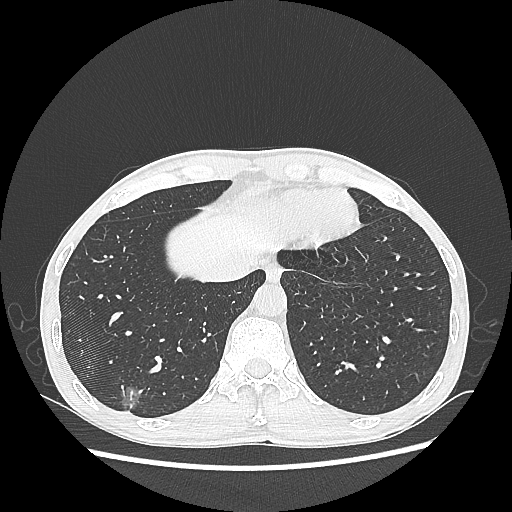
Chest CT, one axial slice; position 66 of 270 along the scan axis; reconstruction kernel LUNG; 100 kVp; lung window (W 1500 / L -600 HU); 512 × 512 image matrix. Patient: male, 60 years. Case-level facts recorded for this patient, not image findings: clinical TNM (as recorded): T1c N0 M0; histopathological grade: G2.
Structures marked on this image (rectangle marked by the reading radiologist):
- lung tumour (recorded histology: adenocarcinoma): bounding box (x1, y1, x2, y2) in pixels: (115, 377, 145, 421)